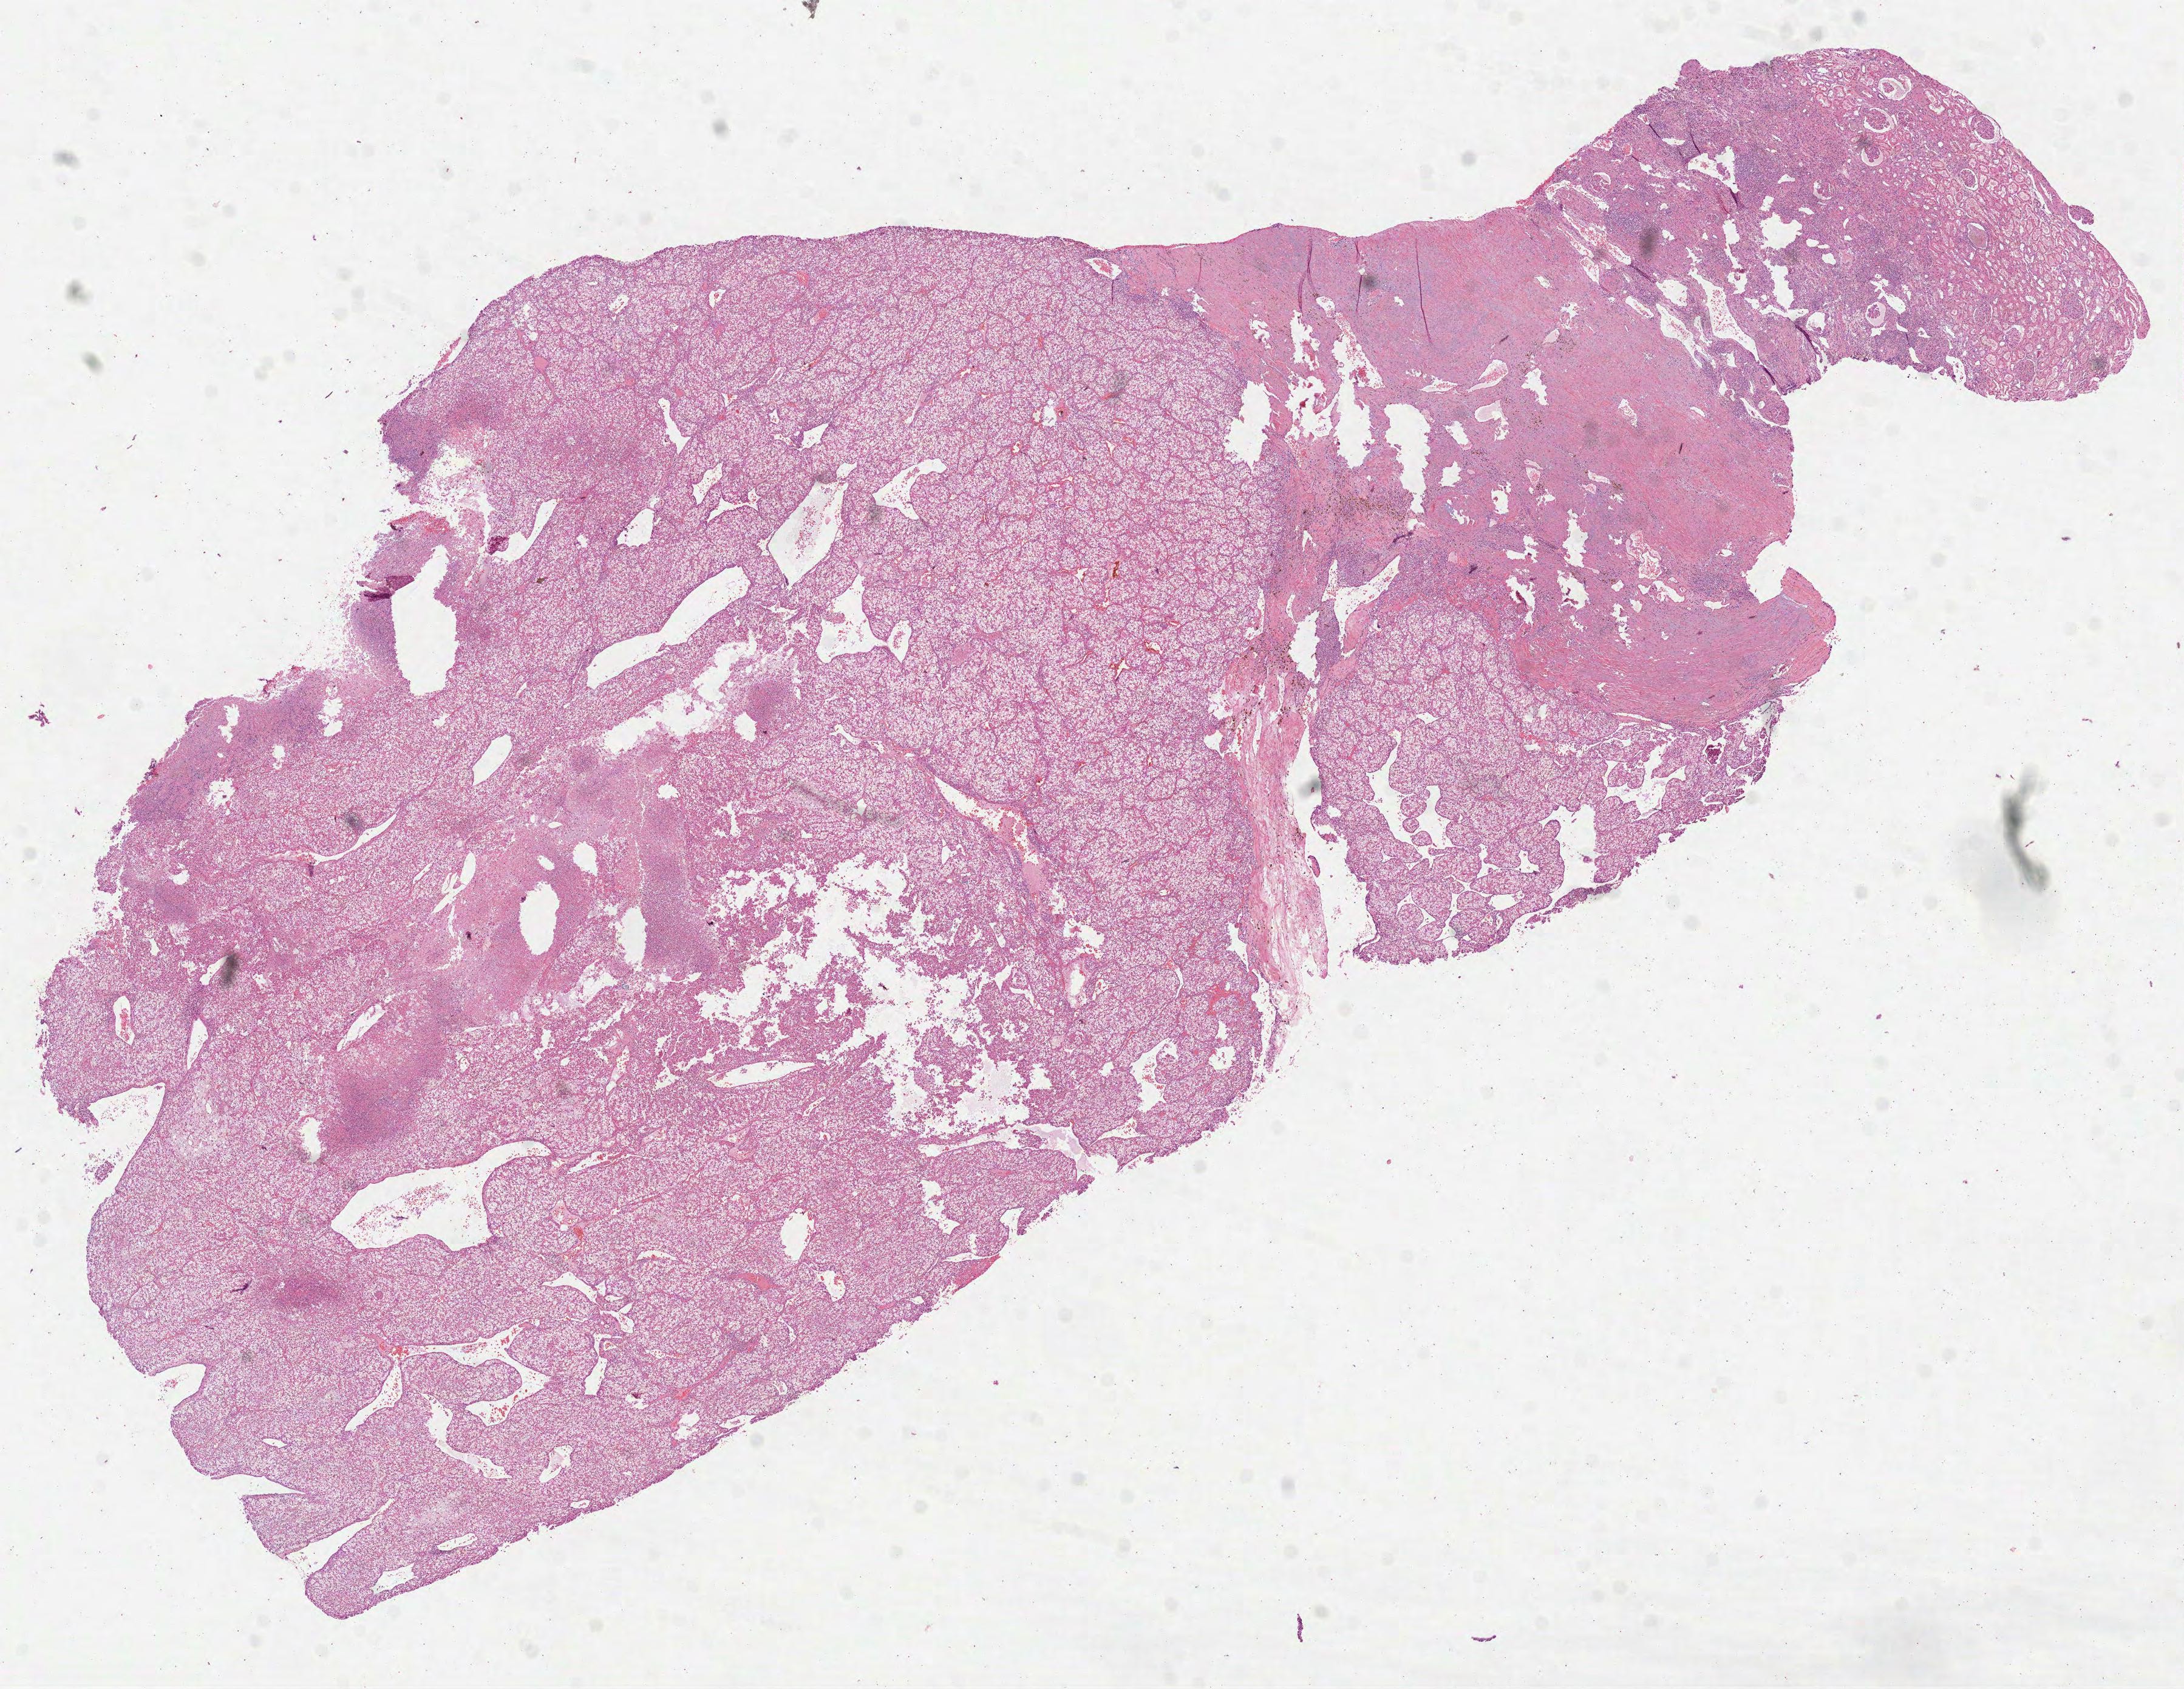
H&E whole-slide image, low-resolution overview of the scanned area, about 14.5 x 11.2 mm (from a 40x scan), formalin-fixed paraffin-embedded (FFPE) diagnostic section, primary tumour sample from the kidney. Male, age 60 years at initial diagnosis. Histologic grade: G3 (poorly differentiated).
Histologic diagnosis: Clear cell adenocarcinoma, NOS. AJCC pathologic stage: I.